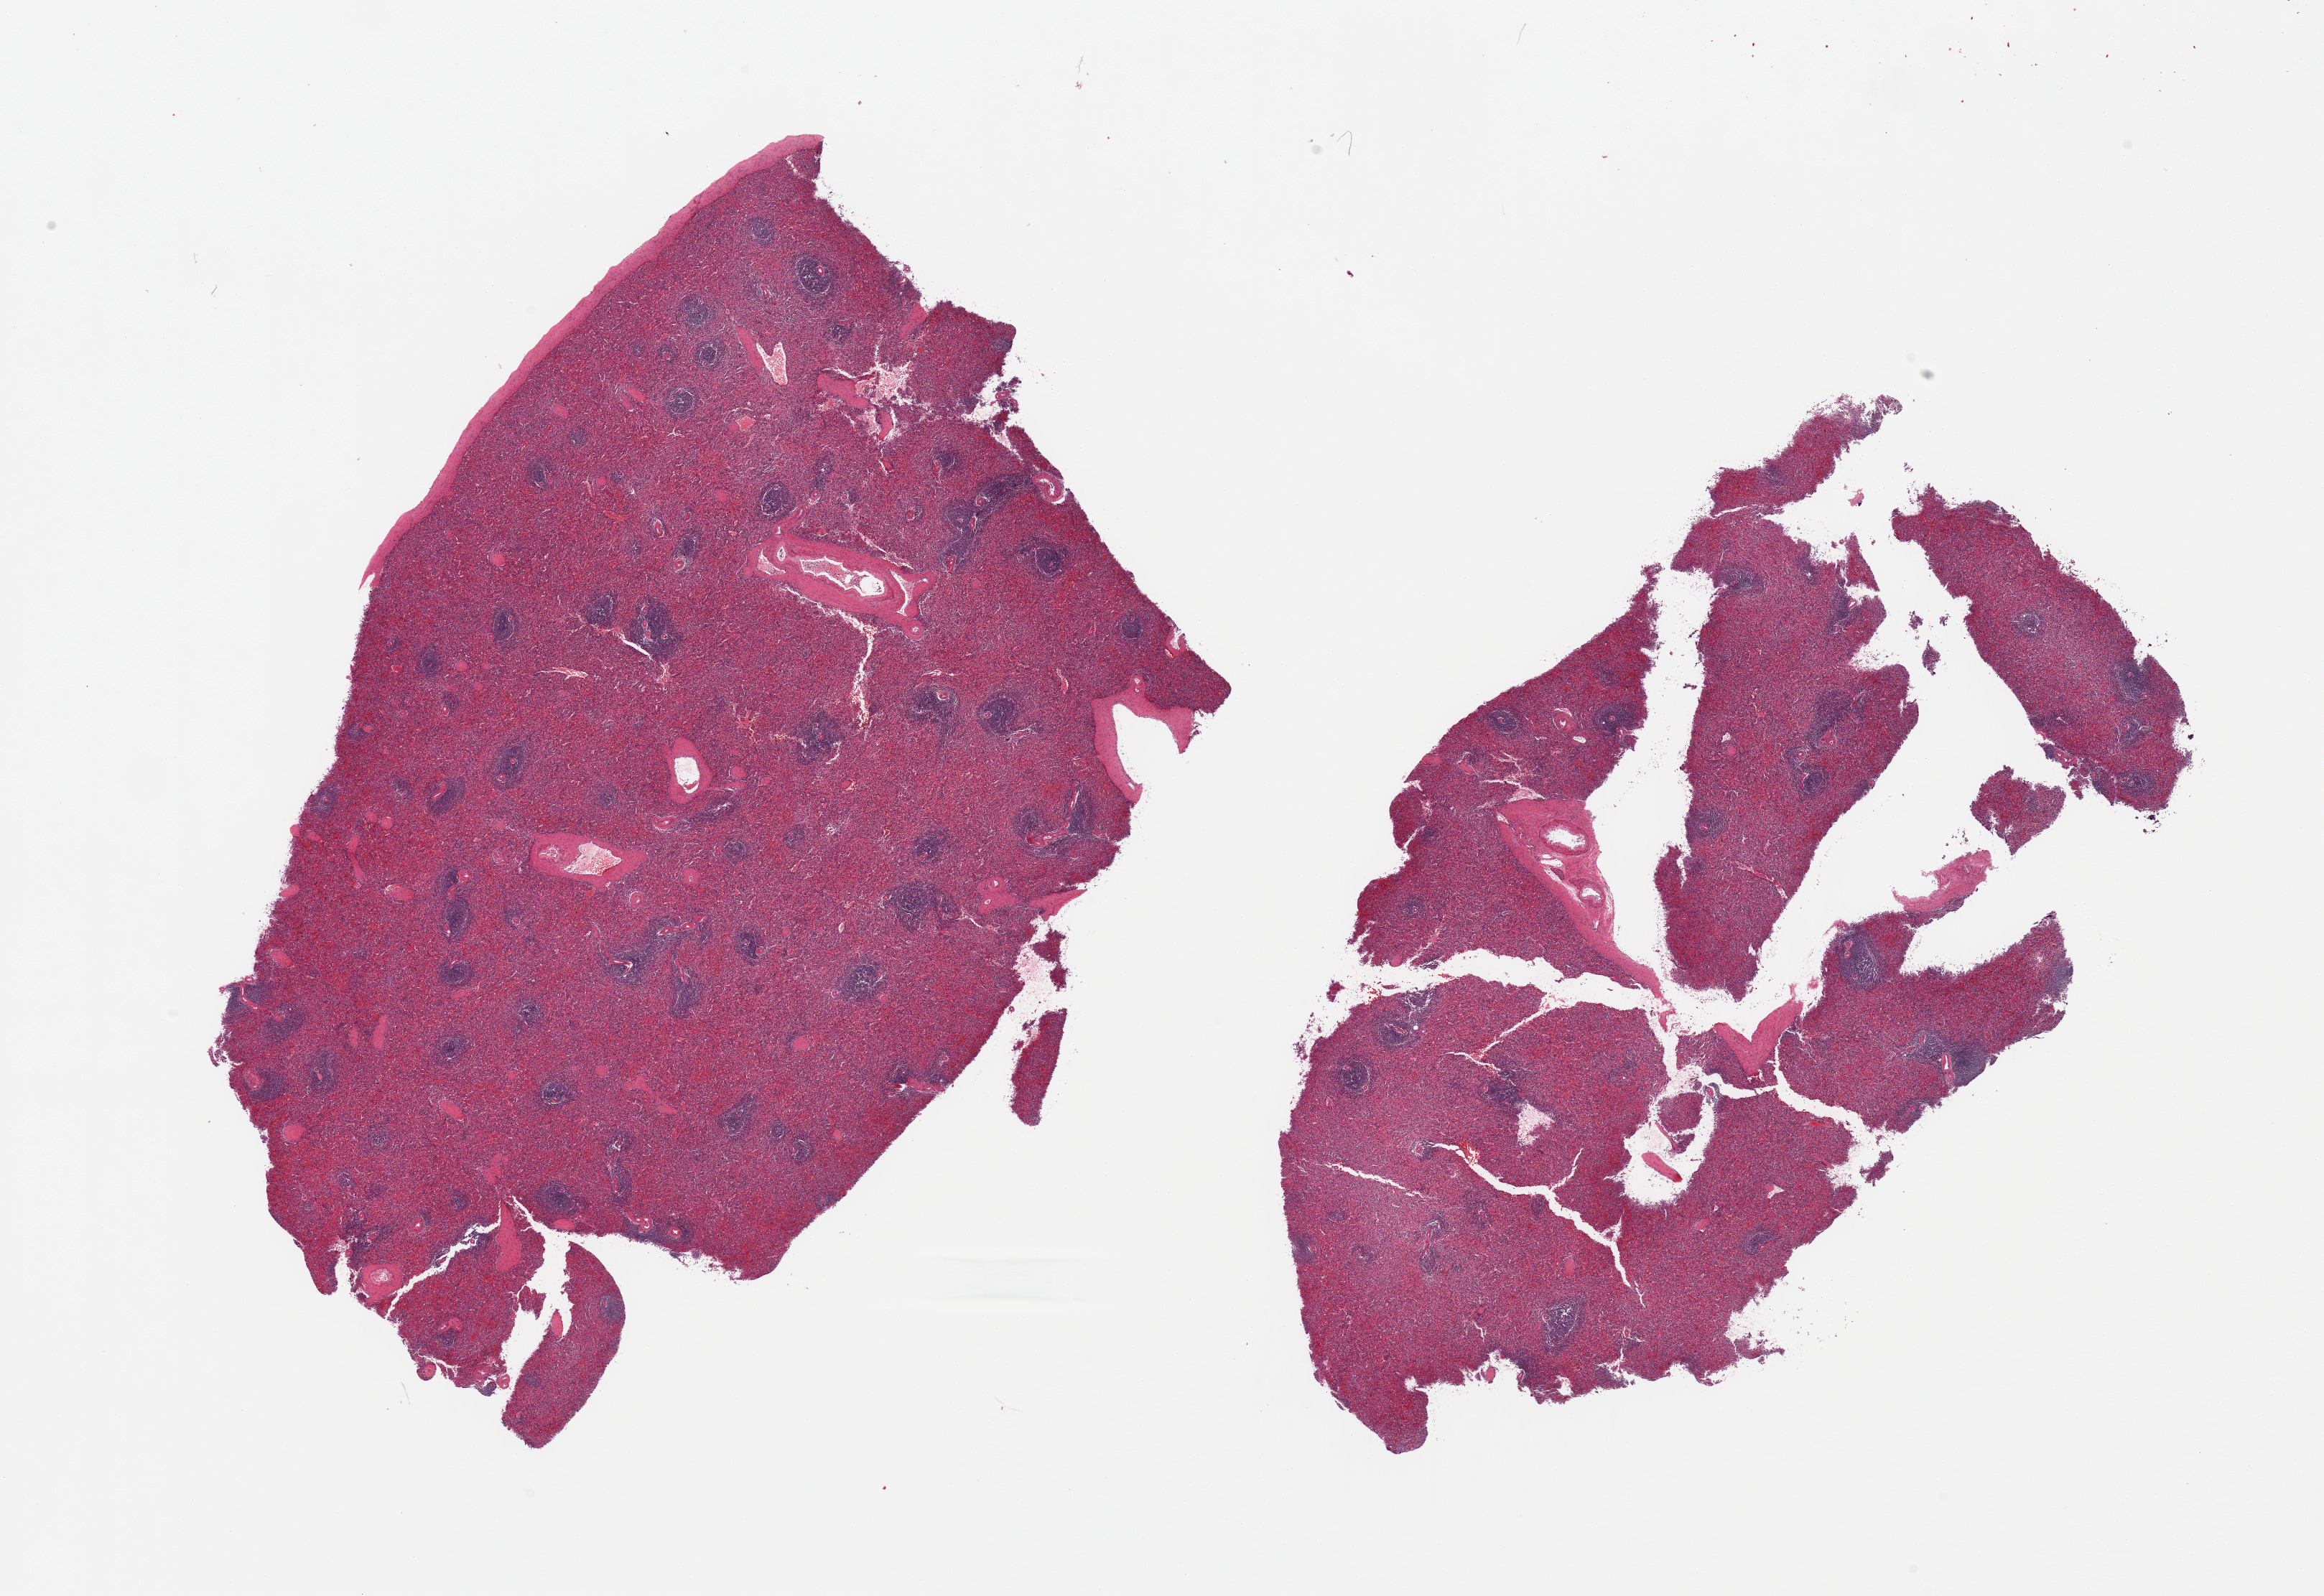
Digitized hematoxylin and eosin (H&E)-stained section — a low-resolution overview of the entire scanned area, about 25.6 x 17.6 mm, PAXgene-fixed, paraffin-embedded tissue, target tissue: spleen, tissue donor sample. Male donor.
• review note (as recorded): 2 pieces, one includes capsule (should be 5mm below capsule), influx of granulocytes within red pulp